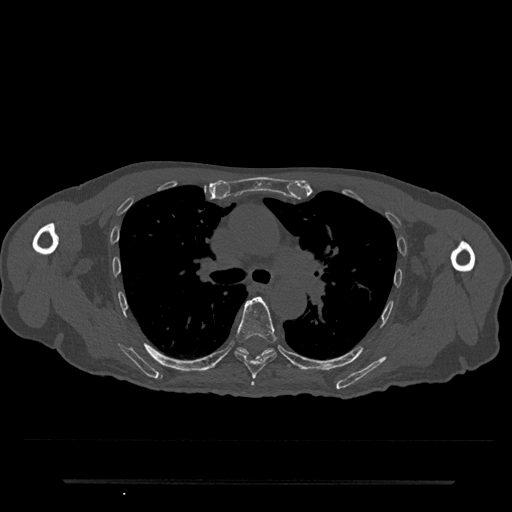
CT including the spine, one axial slice; position 520 of 797 along the scan axis; reconstruction kernel Br40s/3; bone window (W 1800 / L 400 HU); 512 × 512 image matrix, field of view 427 × 427 mm. Patient: male, 74 years. Case-level facts recorded for this patient, not image findings: primary cancer: prostate.
Outlined on this slice (semi-automatically segmented with operator editing):
- T5 vertebra: bounding box <251,382,255,386> (left, top, right, bottom; pixels)
- T6 vertebra: <234,296,278,379>
- T7 vertebra: <238,347,290,368>